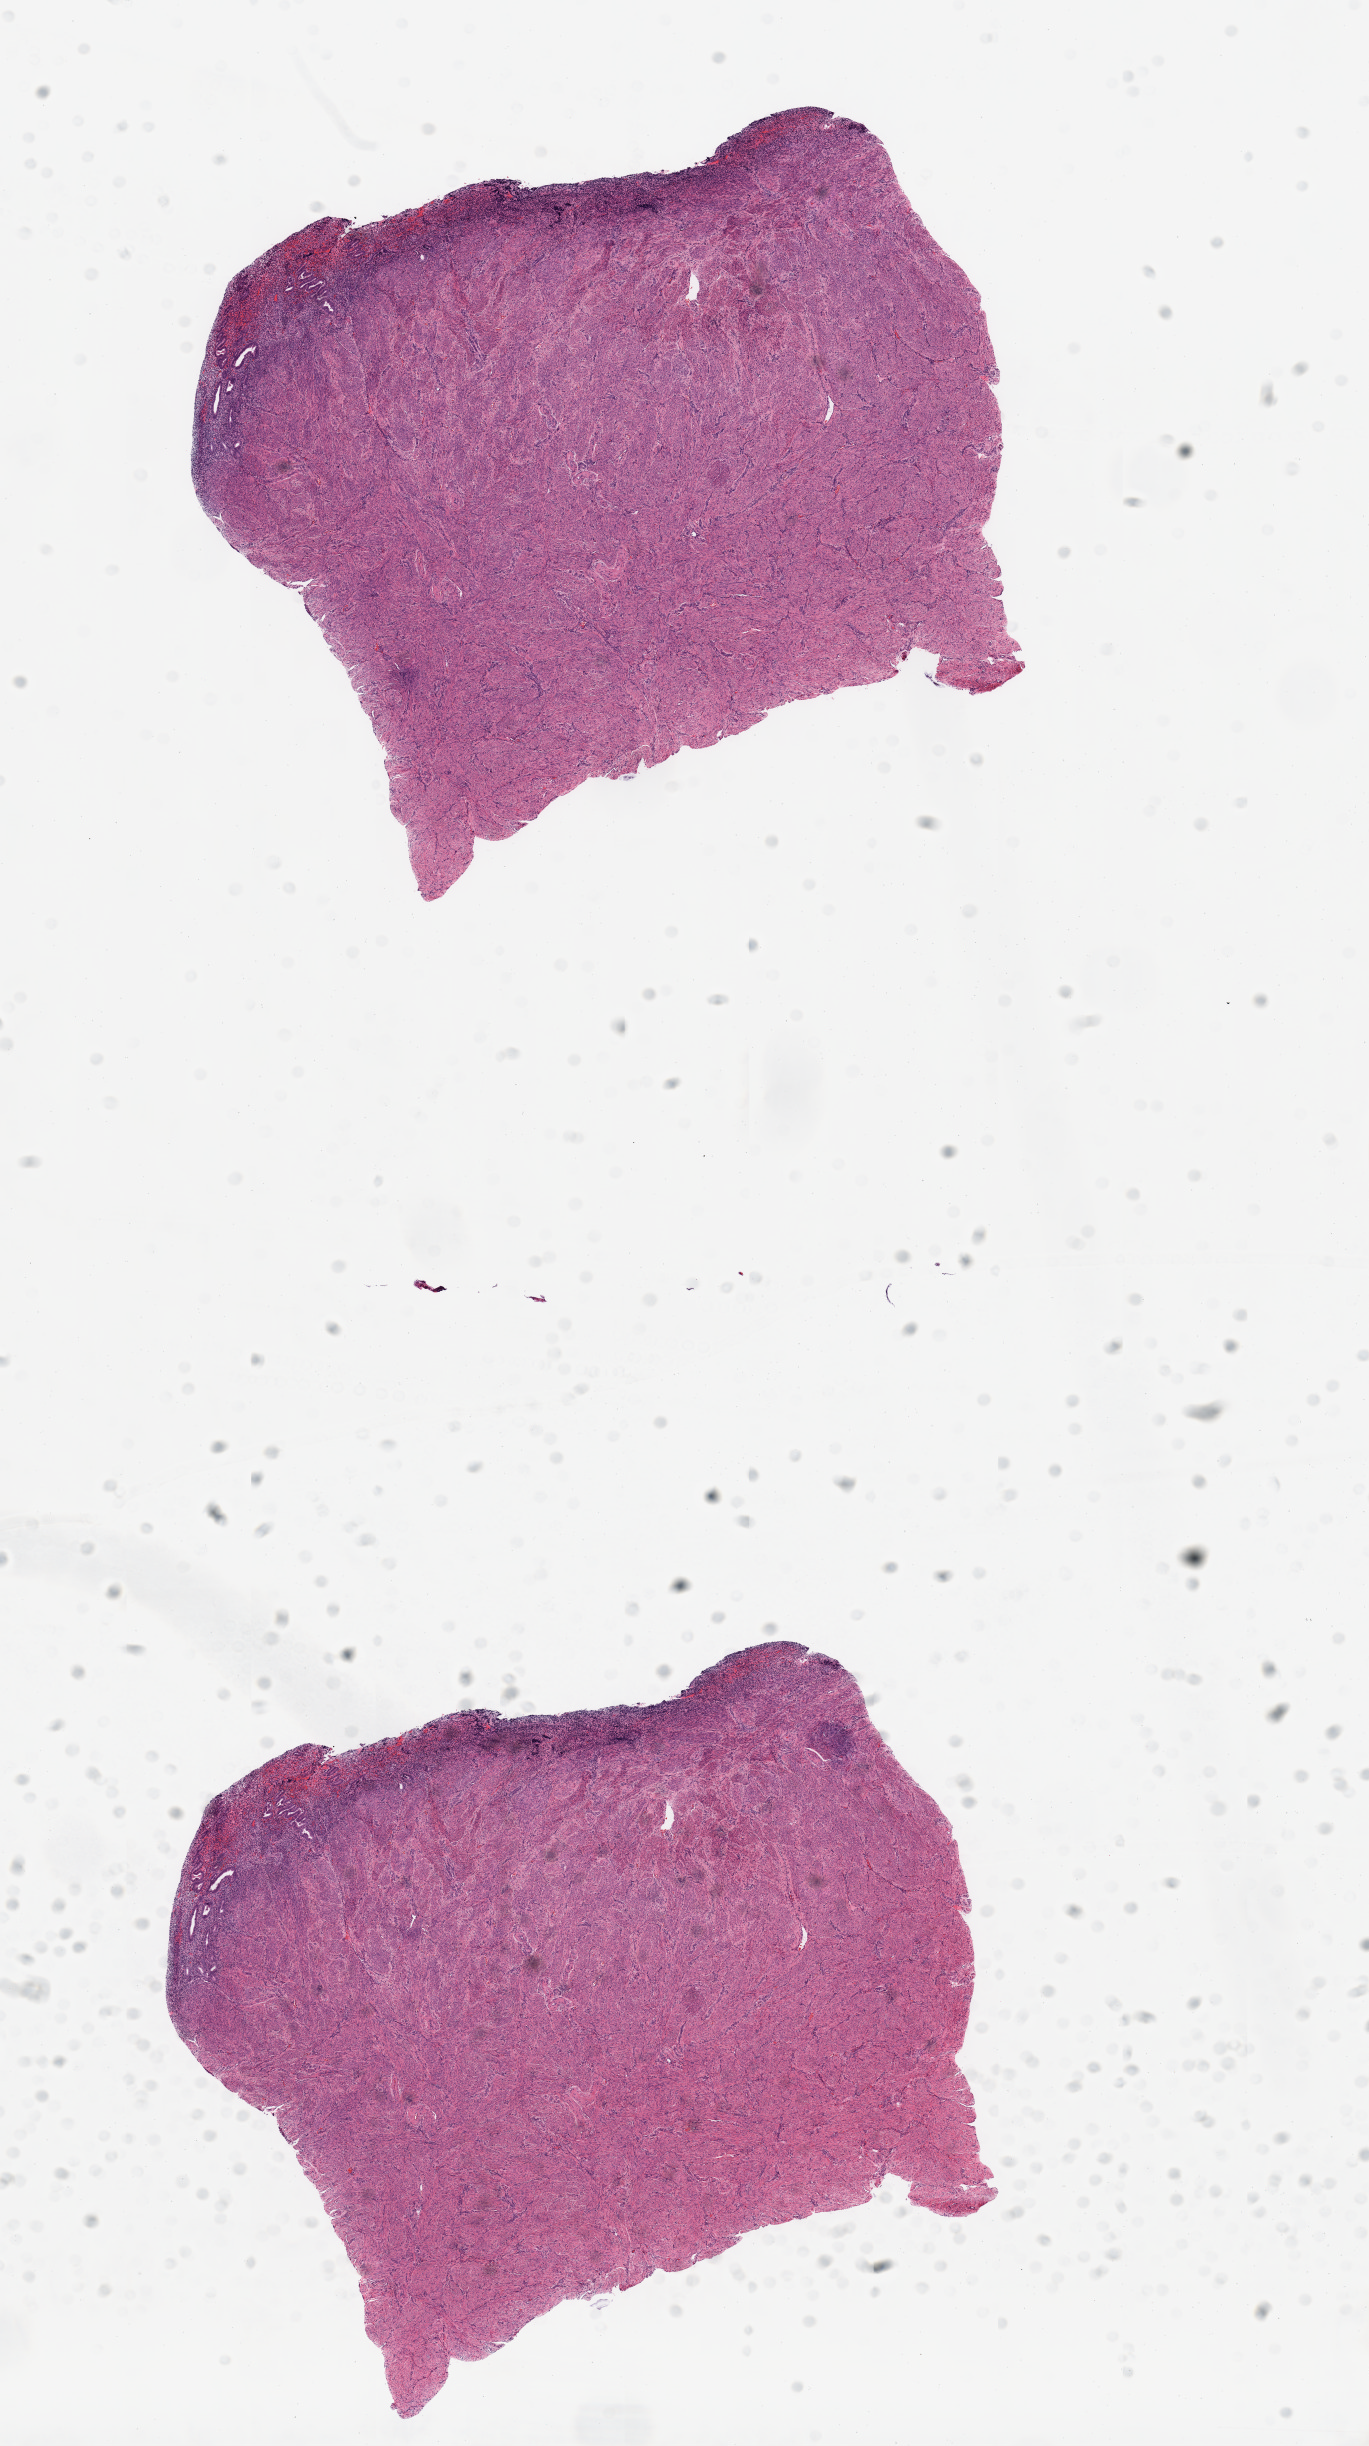
Whole-slide histology image, H&E — shown as a low-resolution overview of the whole scanned area (about 10.8 x 19.3 mm), normal (non-tumour) tissue sample, sampled site: uterus. Patient: female, age 55 years.
- this section: normal (non-tumour) tissue from the same patient
- patient diagnosis: Endometrioid adenocarcinoma, NOS